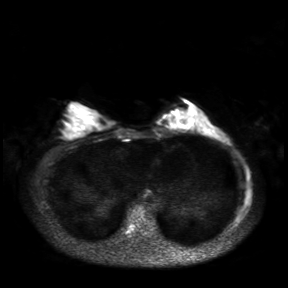
Breast MRI, one axial slice; position 13 of 30 along the scan axis; diffusion-weighted series; image 2 of 4 stored at this slice position (different b-values; order by instance number); 3 T; 4 mm slice thickness; 288 × 288 image matrix. Female patient.
Outlined on this slice (manually delineated by an expert):
- tumour on diffusion-weighted imaging: box from (x=163, y=114) to (x=173, y=120) px